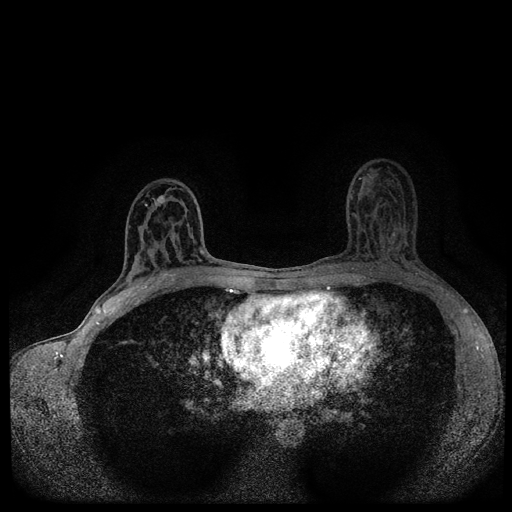
Breast MRI (dynamic contrast-enhanced, multi-phase), one axial slice. Slice 56 of 116 in the series (ordered by position). Dynamic contrast-enhanced series, time point 2 of 5 at this slice position (early post-contrast). 1.5 T. TE 2.7 ms, TR 5.4 ms. 512 × 512 image matrix, field of view 320 × 320 mm. Patient: female, 43 years.
Structures marked on this image (semi-automatically segmented with operator editing):
- breast lesion (labelled 'tumour' in the annotation; benign lesions carry a separate 'benign' label): bounding box [x1, y1, x2, y2] px = [156, 194, 165, 205]